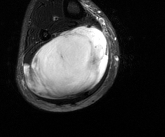
MRI of an extremity soft-tissue mass, one axial slice; position 58 of 81 along the scan axis; T2-weighted fat-saturated; MR volume resampled by the dataset authors to the PET/CT grid (not the native acquisition matrix); 3.27 mm slice thickness; 165 × 137 image matrix, field of view 161 × 134 mm. Male patient. From the clinical record (not read from this slice): histological type: liposarcoma - round cell; grade: high; site of the primary tumour: right calf.
Outlined on this slice (expert contour drawn on MRI and transferred to this co-registered scan by the dataset authors):
- gross tumour volume (mass): bounding box (x1, y1, x2, y2) in pixels: (23, 25, 109, 99)